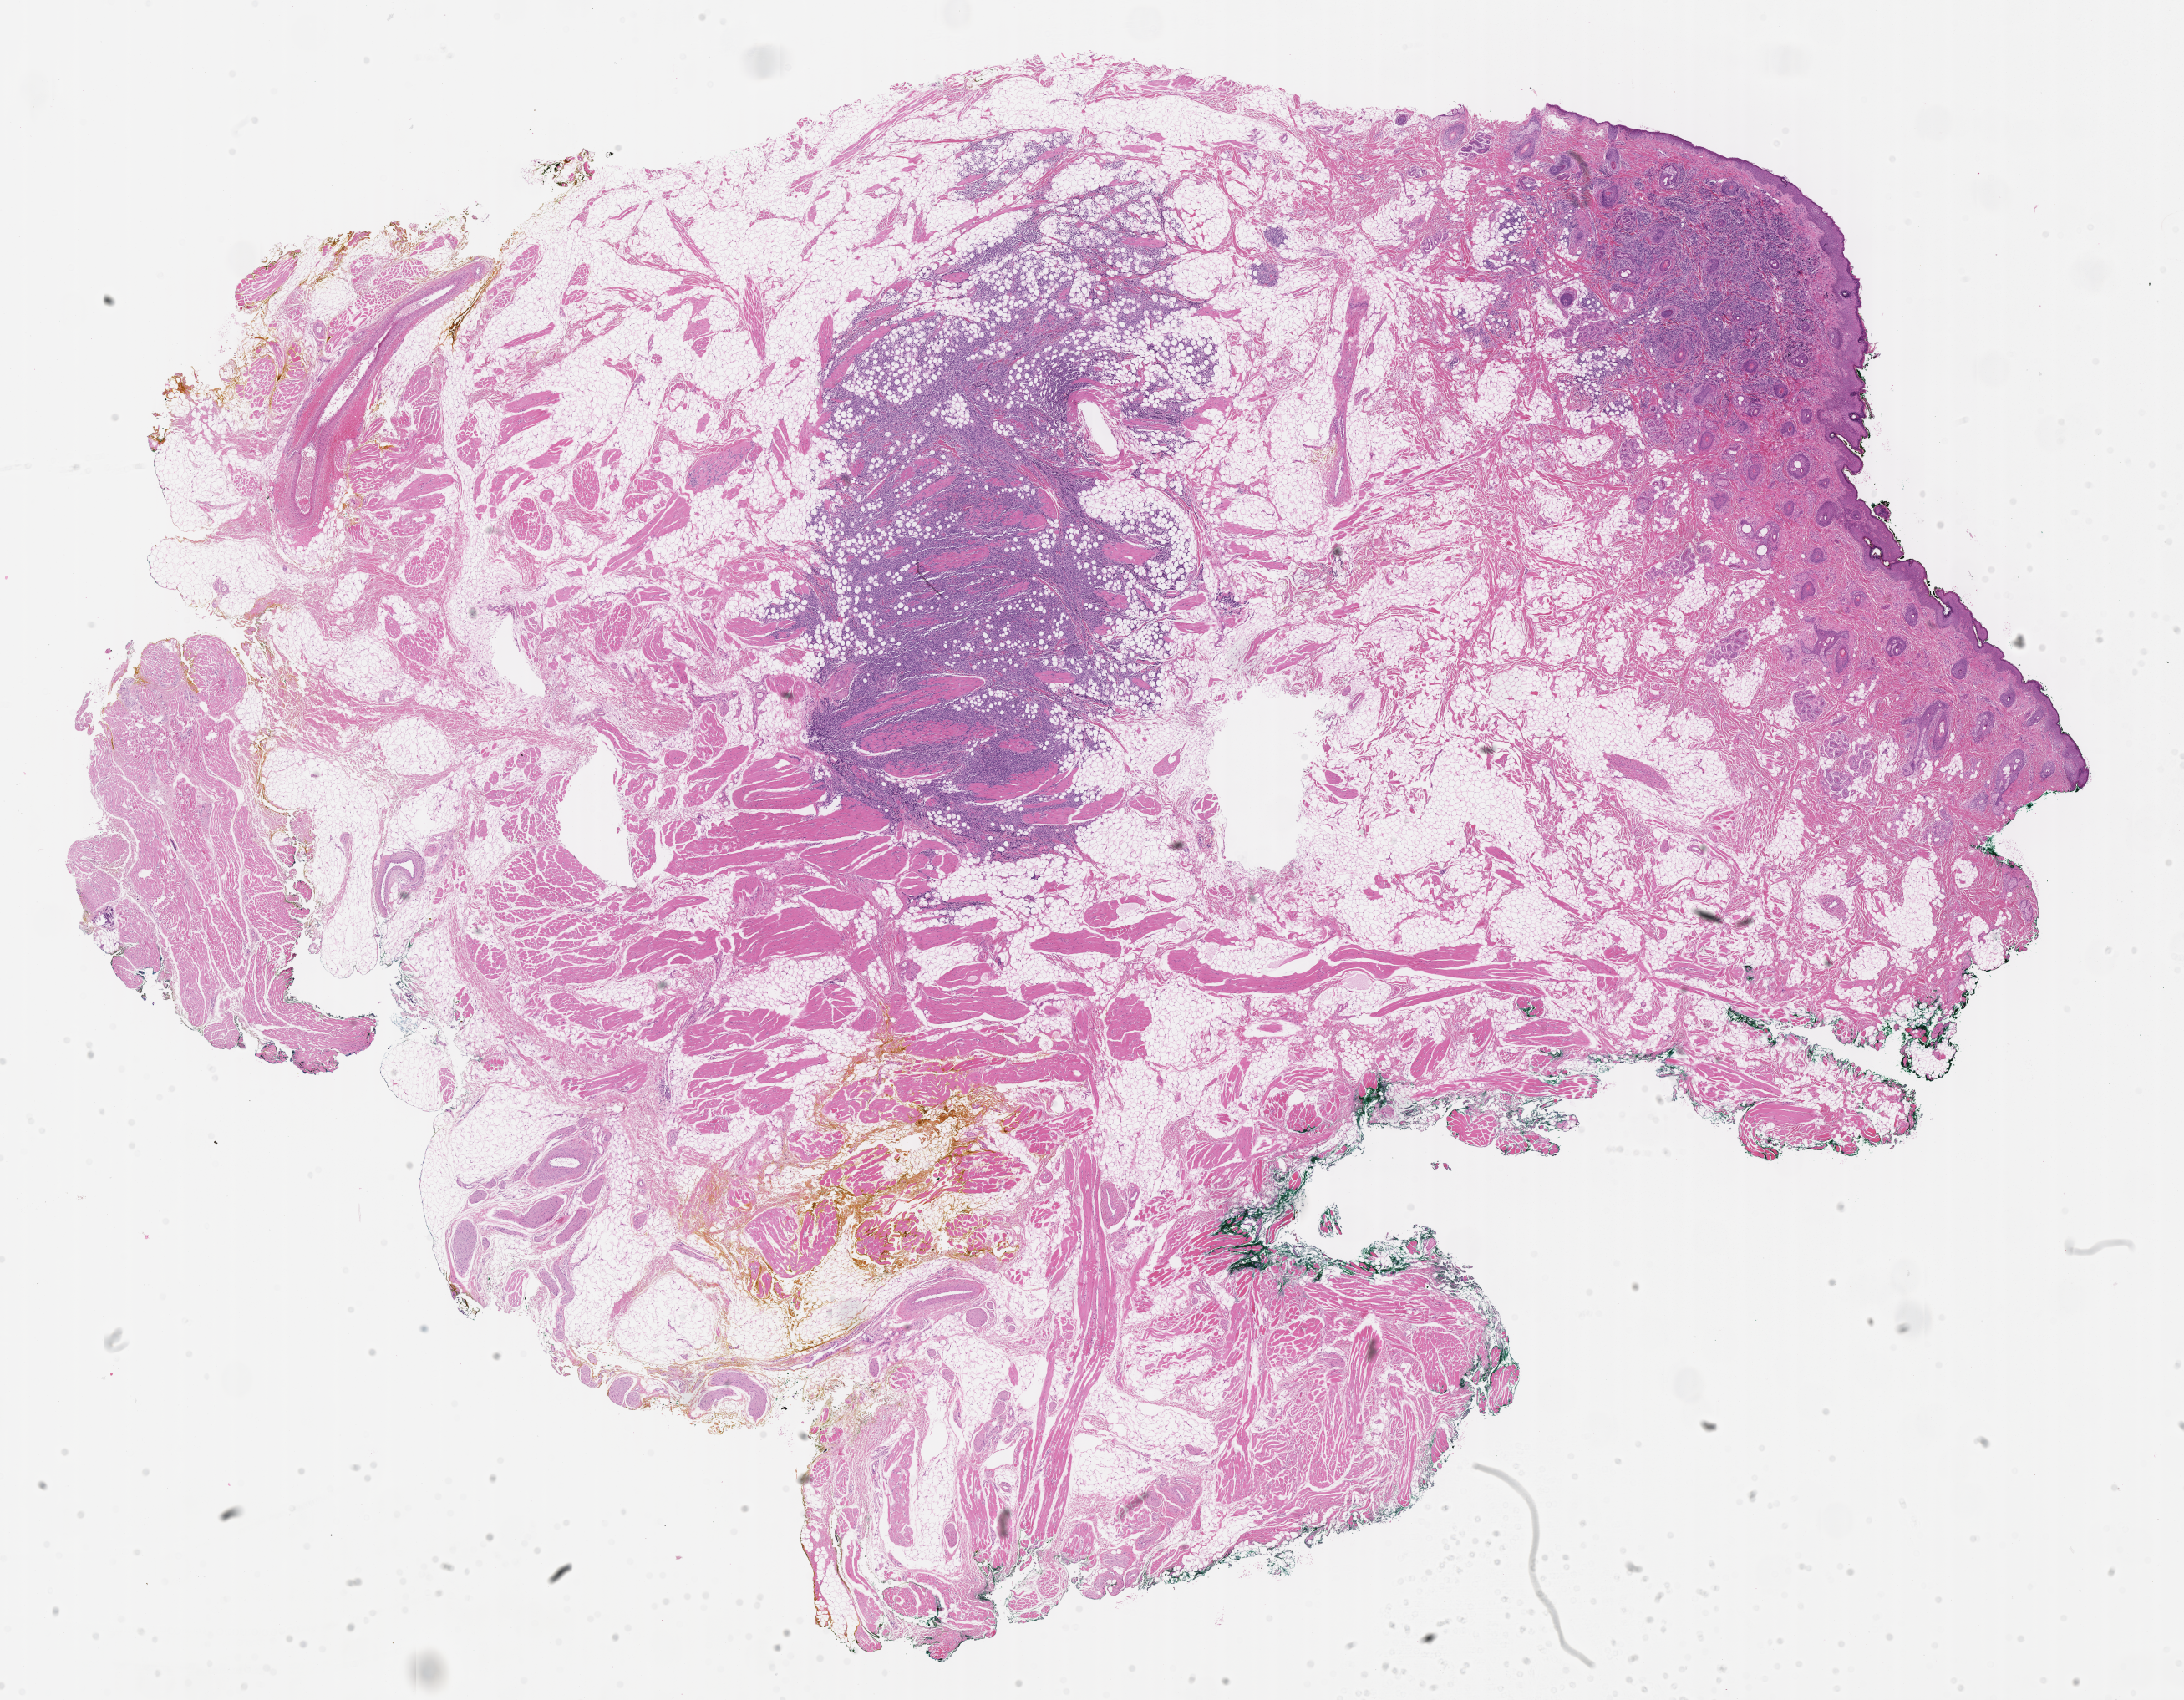
Digitized haematoxylin and eosin-stained section of tumor tissue — whole scanned area (about 21.1 x 16.5 mm) shown as a low-resolution overview, FFPE section, sample anatomic site: chin. Patient: male, age 3.3 years at diagnosis.
- stage (as recorded): 1
- diagnosis: rhabdomyosarcoma; histological classification: embryonal rhabdomyosarcoma